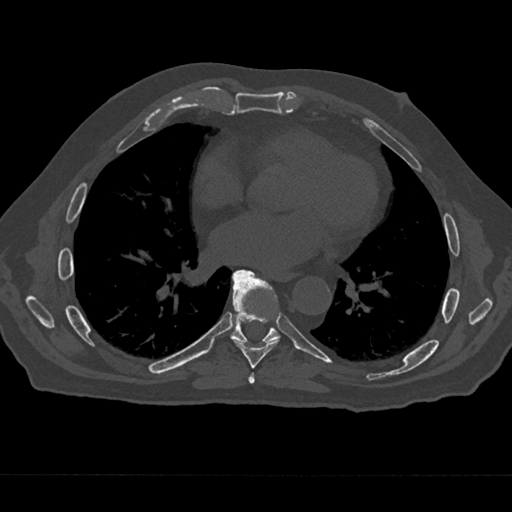
CT including the spine, one axial slice. Slice 347 of 797 in the series (ordered by position). Reconstruction kernel Br40s/3. 120 kVp. Bone window (W 1800 / L 400 HU). 0.5 mm slice thickness. 512 × 512 image matrix, field of view 377 × 377 mm. Patient: male, 75 years. Case-level facts recorded for this patient, not image findings: primary cancer: renal; vertebrae with lytic lesions (as recorded): T4.
Annotated regions visible in this slice (semi-automatic segmentation, software-assisted and operator-edited):
- T6 vertebra: bounding box (x1, y1, x2, y2) in pixels: (248, 373, 255, 384)
- T7 vertebra: (233, 269, 280, 369)
- T8 vertebra: (230, 271, 280, 343)